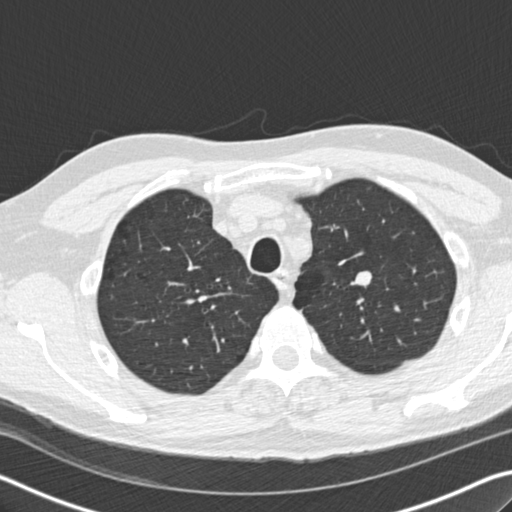
Axial slice from a low-dose chest CT screening exam; baseline screening round; lung window (W 1500 / L -600 HU); 2 mm slice thickness; 512 × 512 image matrix, field of view 340 × 340 mm. Male participant, aged 56 years at enrolment.
Expert reader's lesion annotation, bounding box (x1, y1, x2, y2) in pixels: (335, 261, 390, 304). The exam's reader record, not a measurement of the box and not confirmed to be the same lesion: non-calcified nodule or mass ≥4 mm, left upper lobe, 12 × 10 mm, smooth margins, soft tissue attenuation. Official screen result: positive, change unspecified: nodule(s) >= 4 mm or enlarging nodule(s), mass(es), or other non-specific abnormalities suspicious for lung cancer. Later outcome: lung cancer diagnosed 814 days after this screen — neuroendocrine carcinoma, NOS, left upper lobe, well differentiated (G1), stage IA (AJCC 6th edition), 20 mm at pathology.